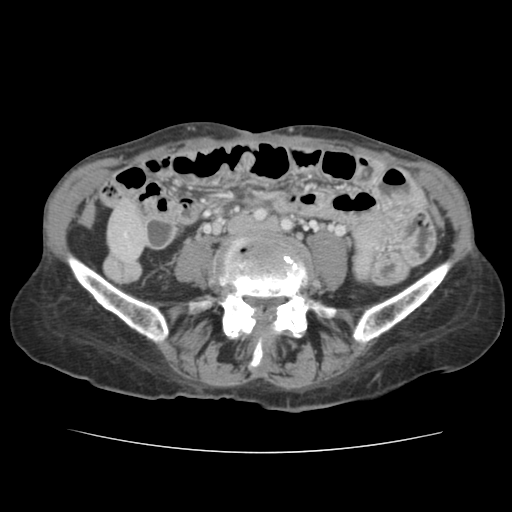
Contrast-enhanced abdominal CT, one axial slice; slice 12 of 136 in the series (ordered by position); intravenous contrast given; soft-tissue window (W 400 / L 40 HU); 2.5 mm slice thickness; 512 × 512 image matrix, field of view 319 × 319 mm. Female patient, age 77 years. Case-level facts recorded for this patient, not image findings: diagnosis: colorectal cancer liver metastases, imaged before liver resection; multiple liver metastases: yes; largest metastasis: 3 cm; disease in both lobes: no.
Structures marked on this image (outlined manually by an expert reader):
- liver: bounding box [x1, y1, x2, y2] px = [110, 208, 145, 260]